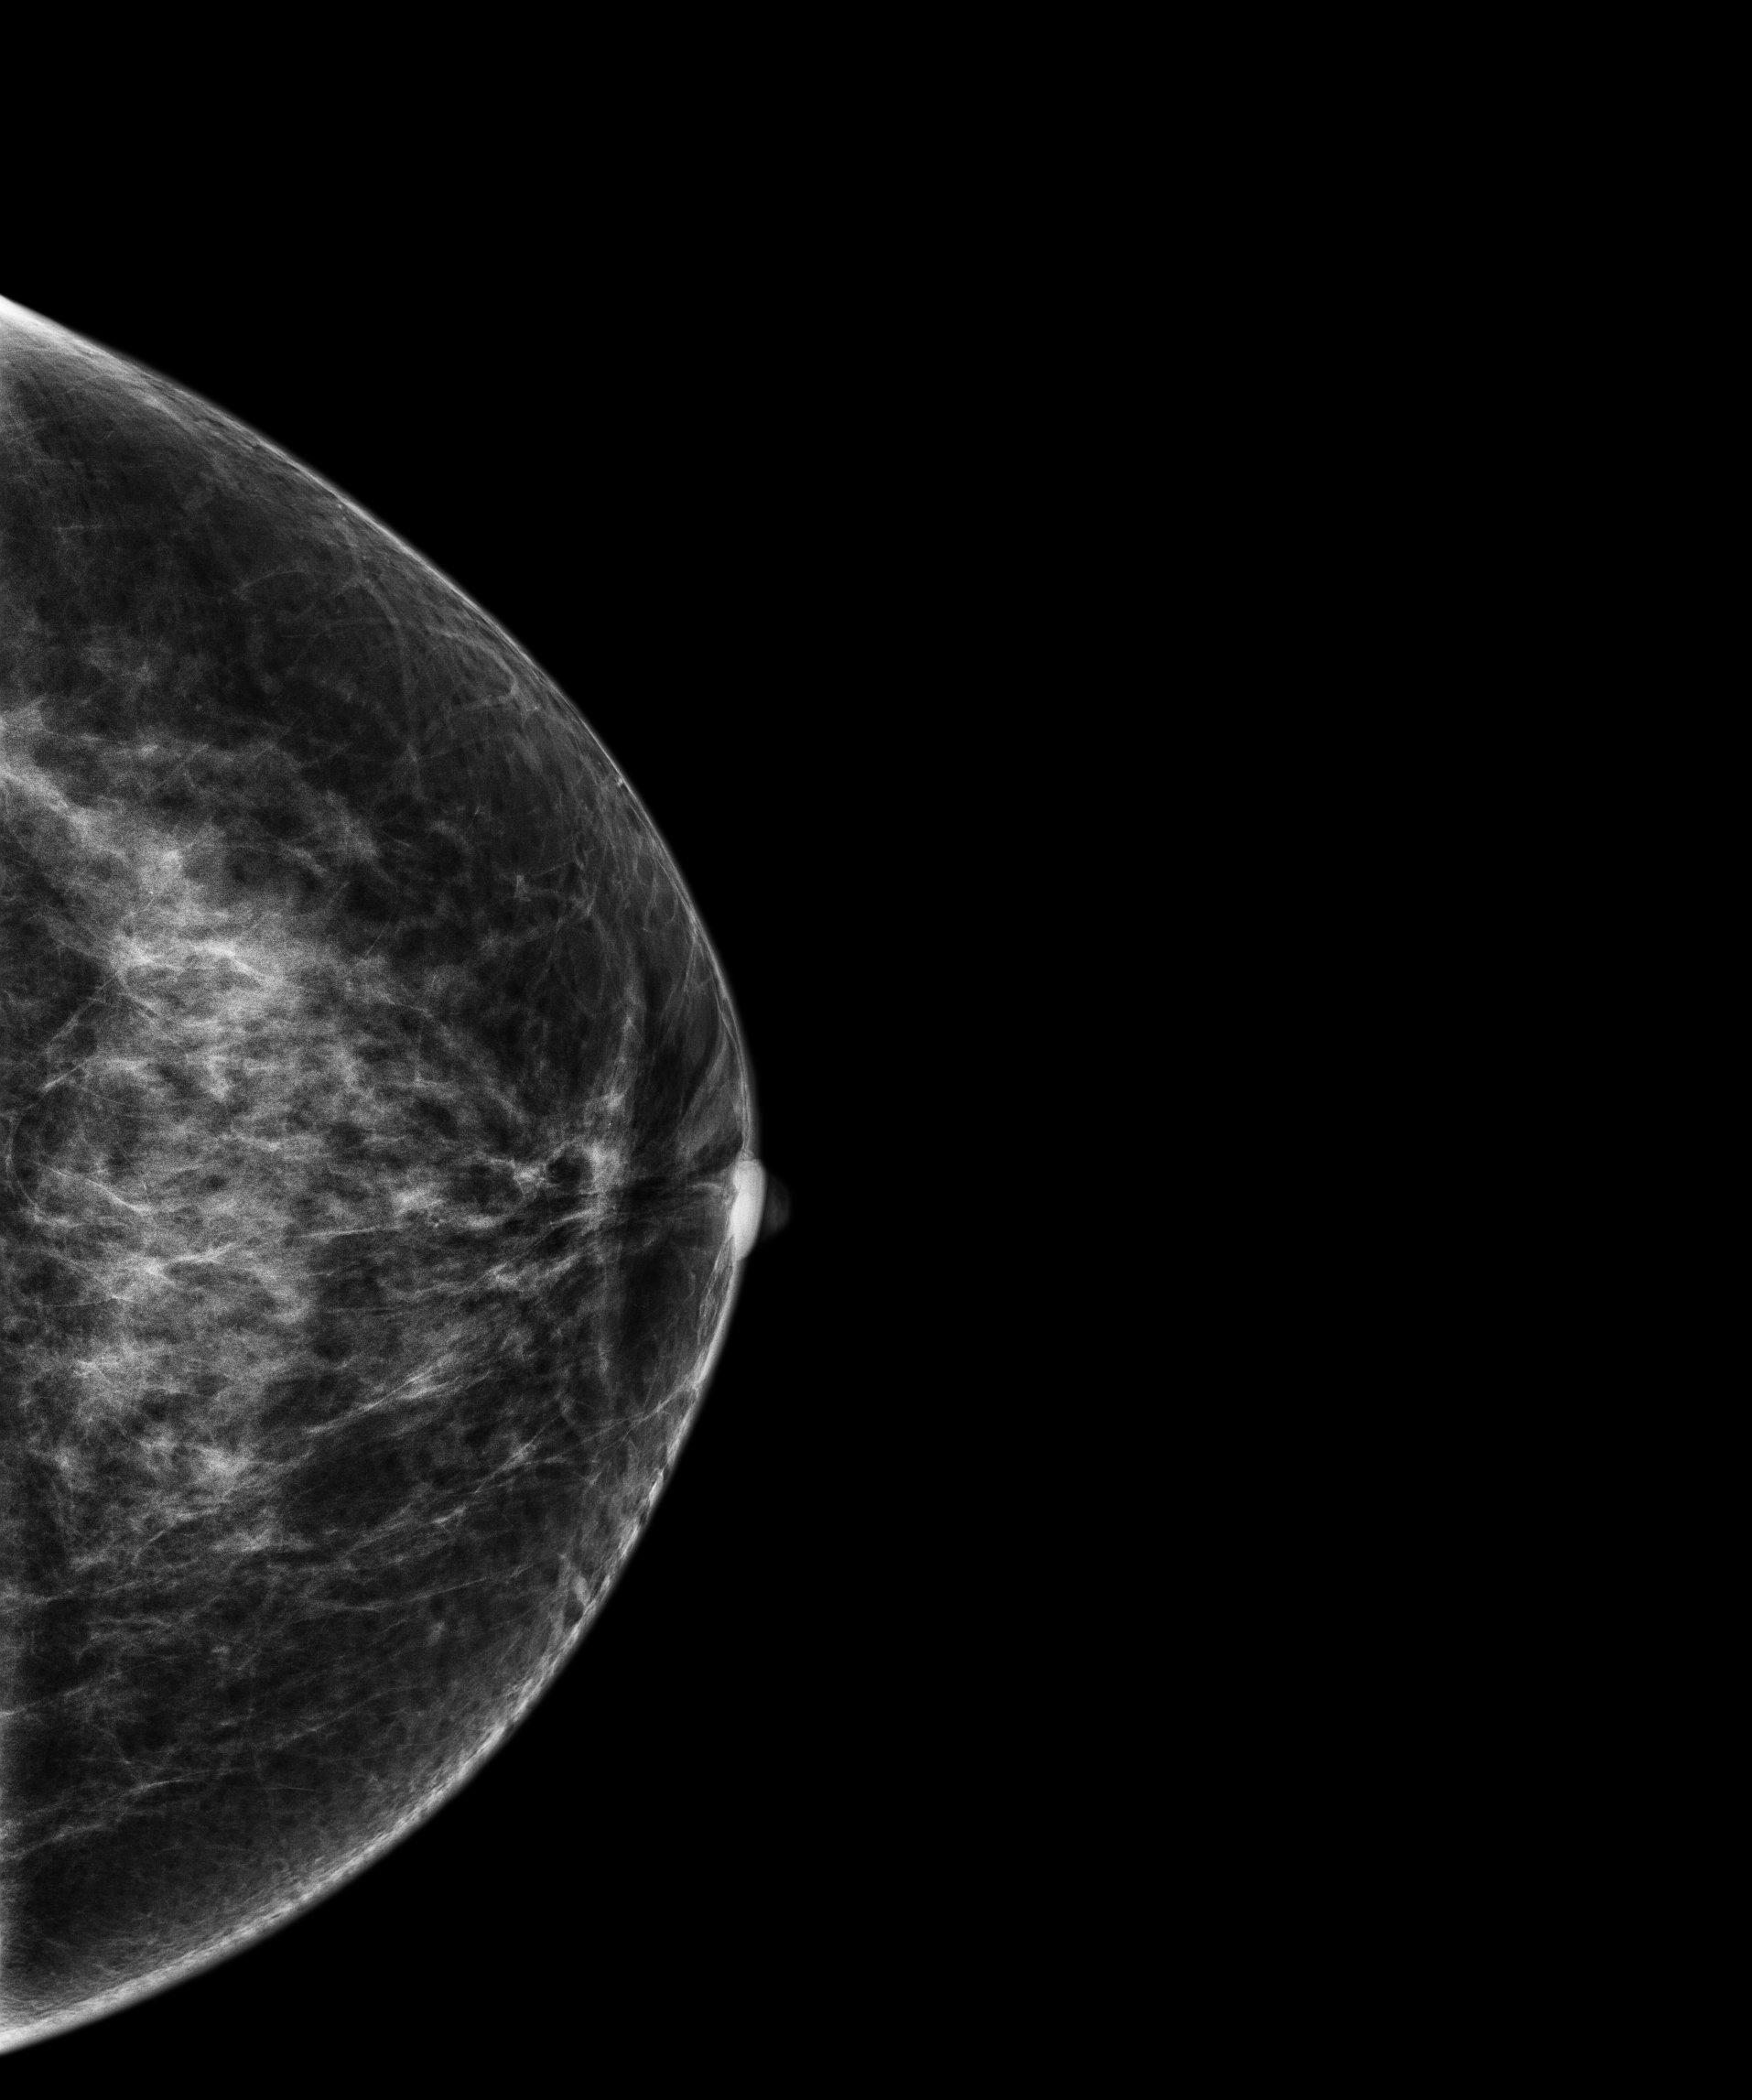
Digital mammogram (FFDM), left breast, CC view, annual screening mammography examination. Patient: female, 48 years.
Breast density at the screening exam (both breasts): heterogeneously dense (BI-RADS density category c). Final BI-RADS assessment for this screening round (tomosynthesis exam, both breasts): category 1. Recall: no recall after this screen.